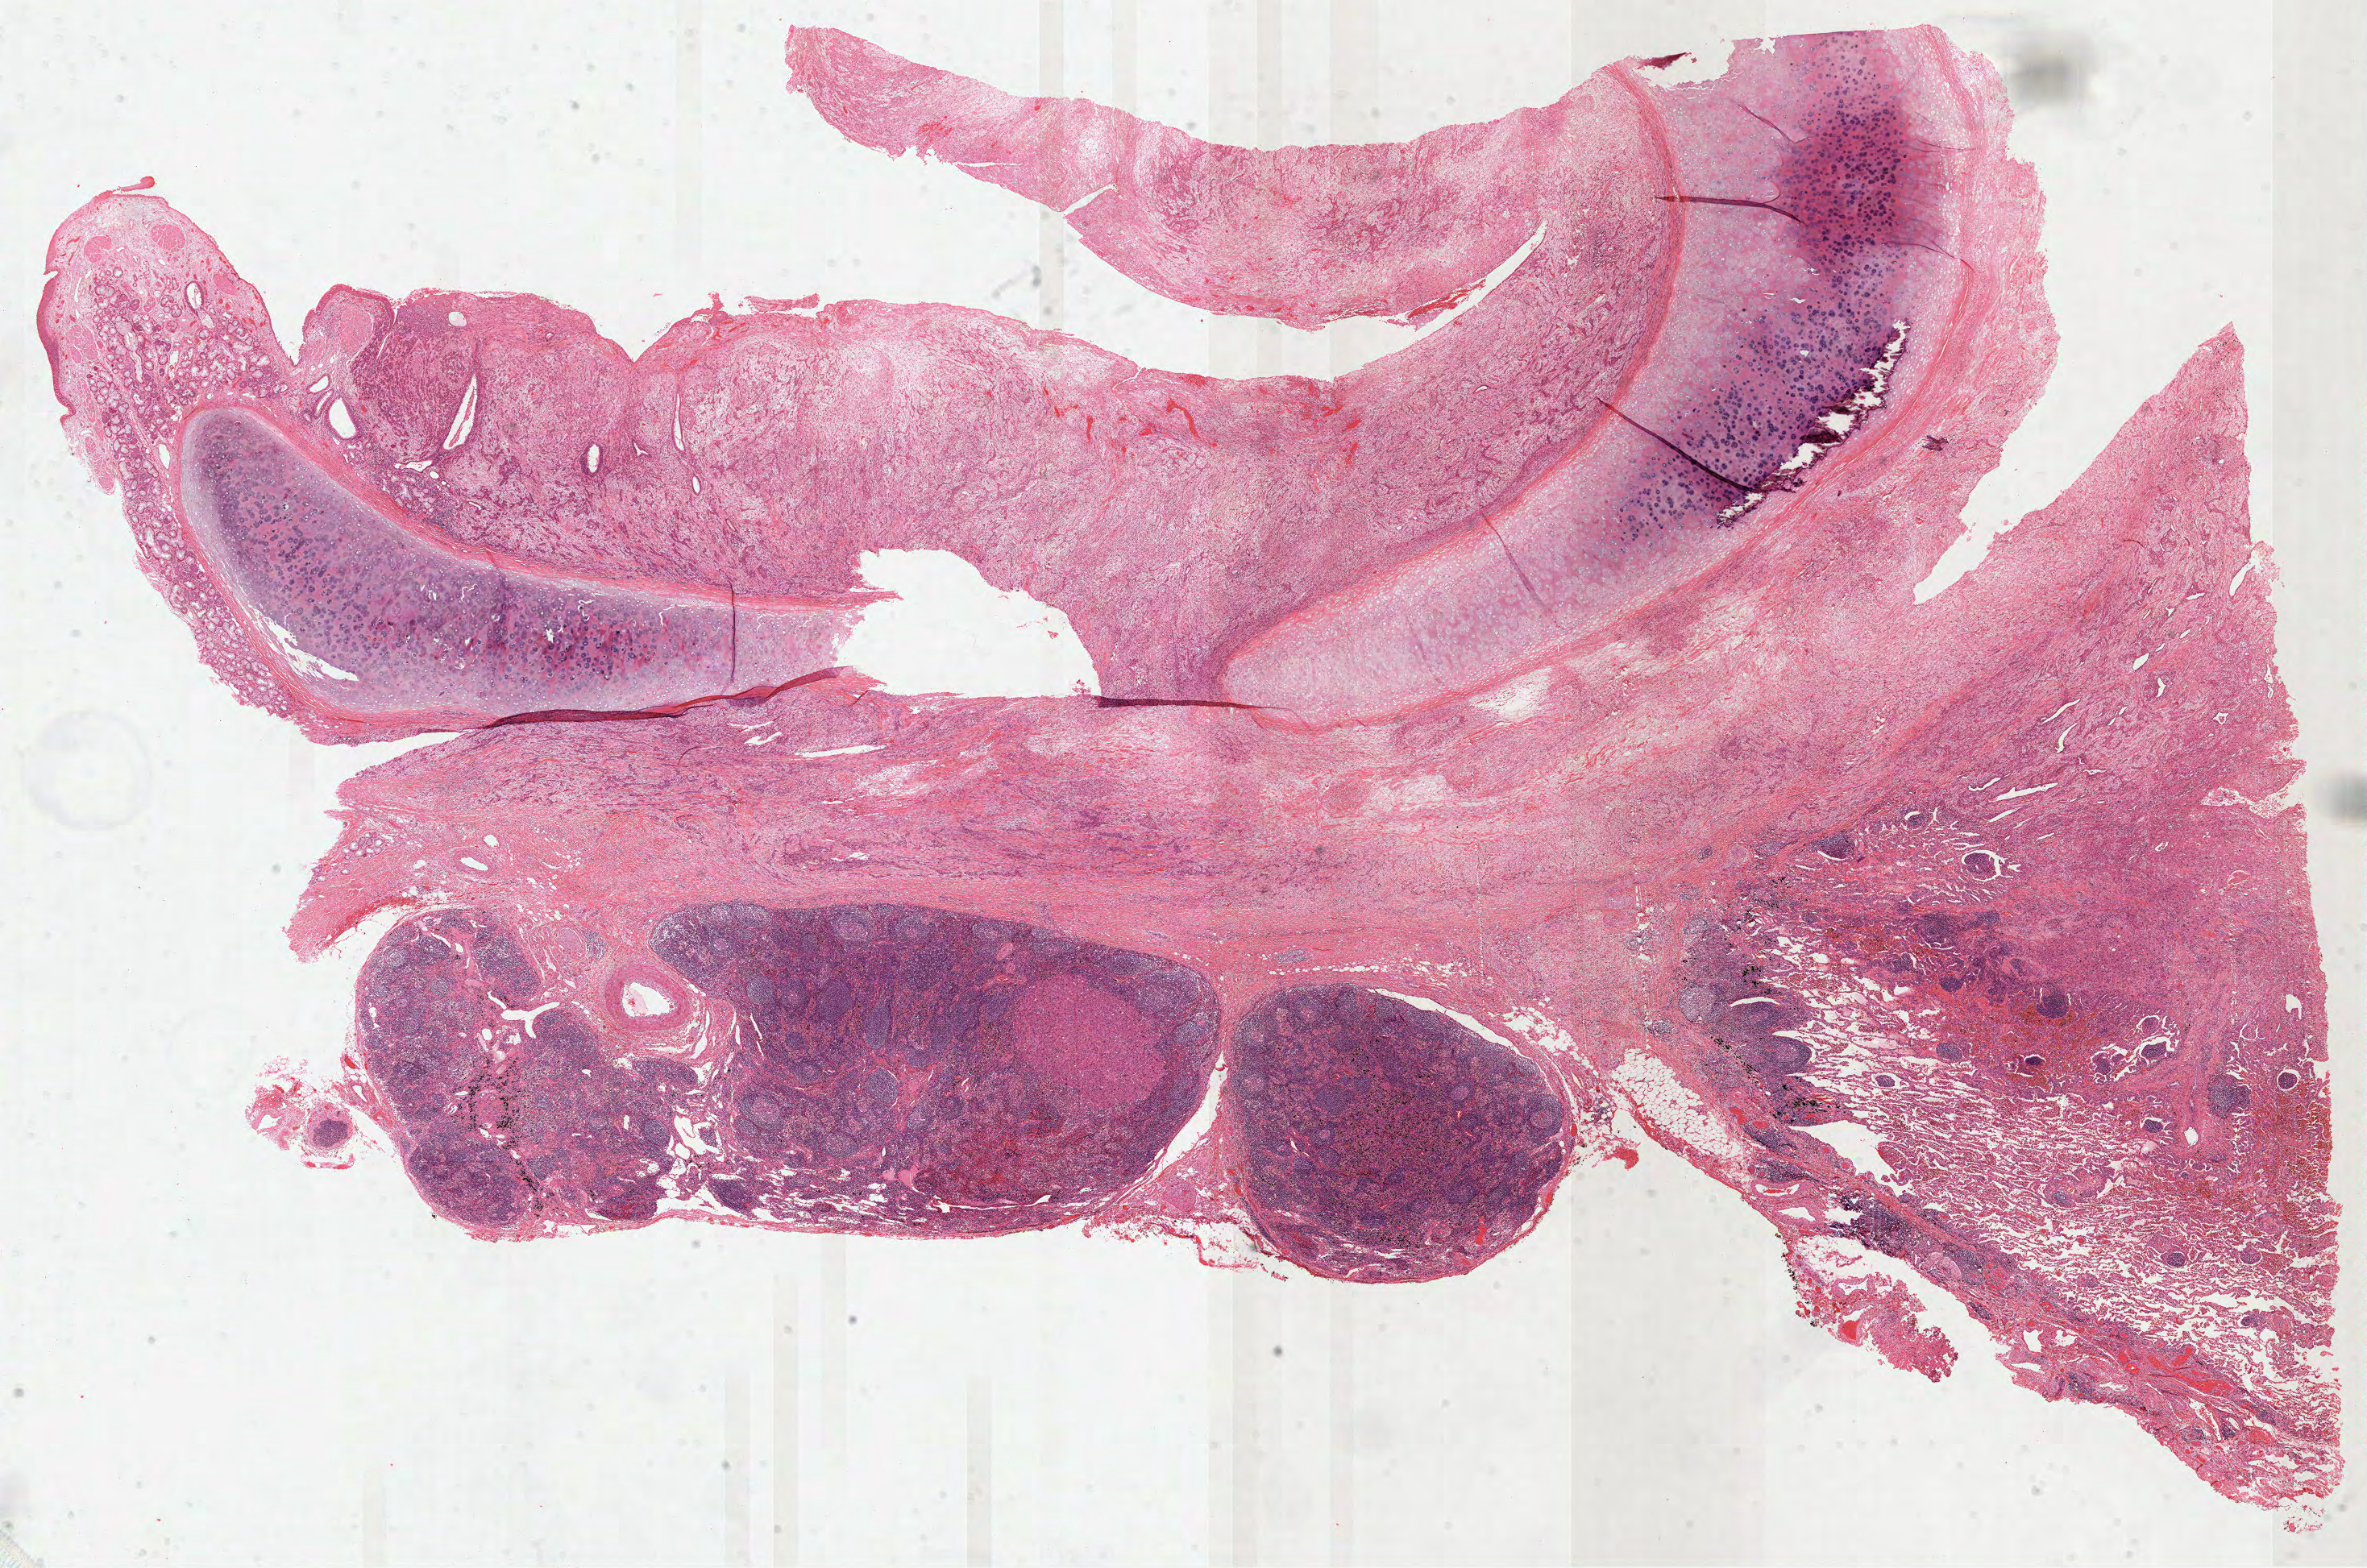
Whole-slide histology image, Hematoxylin and eosin (H&E) stained, whole scanned area (about 23.7 x 15.7 mm, slide scanned at 40x) shown as a low-resolution overview, FFPE section, lung, primary tumour sample. Patient: male, age at initial diagnosis 69 years.
AJCC pathologic stage: IIB (6th edition). Histologic diagnosis: Squamous cell carcinoma, NOS.